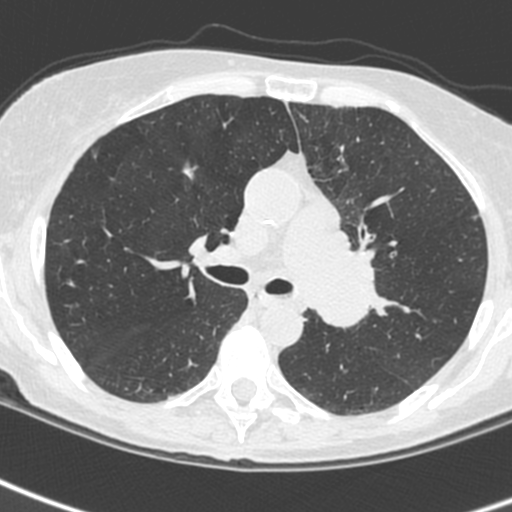
Low-dose screening chest CT, one axial slice. Position 155 of 242 along the scan axis. 120 kVp. Lung window (W 1500 / L -600 HU). 1.3 mm slice thickness. 512 × 512 image matrix, field of view 284 × 284 mm.
Annotated regions visible in this slice (expert manual segmentation):
- lesion 3 (tumor, upper lobe of left lung): bounding box [x1, y1, x2, y2] px = [311, 204, 378, 328]